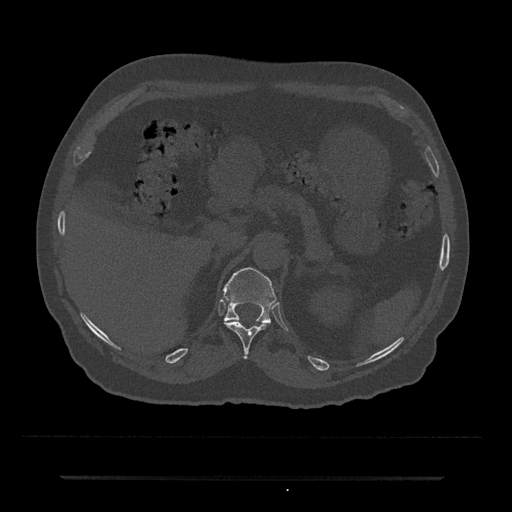
CT including the spine, one axial slice; position 154 of 797 along the scan axis; reconstruction kernel Br40s/3; 120 kVp; bone window (W 1800 / L 400 HU); 0.5 mm slice thickness; 512 × 512 image matrix. Patient: male, 69 years. Case-level facts recorded for this patient, not image findings: primary cancer: prostate.
Annotated regions visible in this slice (semi-automatic segmentation, software-assisted and operator-edited):
- T11 vertebra: bounding box <225,321,267,358> (left, top, right, bottom; pixels)
- T12 vertebra: <222,267,276,324>